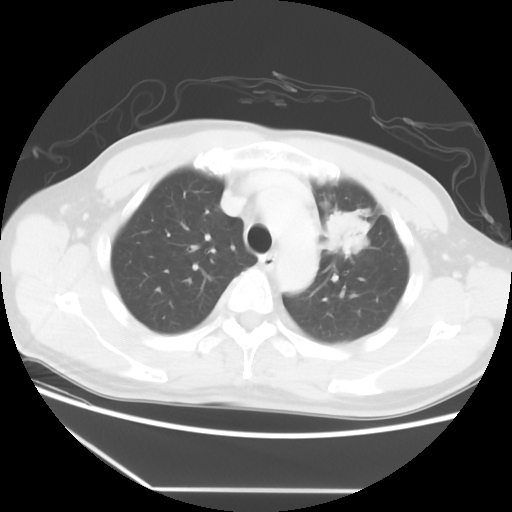
Chest CT, one axial slice; slice 42 of 56 in the series (ordered by position); reconstruction kernel STANDARD; 120 kVp; lung window (W 1500 / L -600 HU); 5 mm slice thickness; 512 × 512 image matrix, field of view 373 × 373 mm. Patient: male, 53 years. Case-level facts recorded for this patient, not image findings: clinical TNM (as recorded): T2a N1 M1b.
Annotated regions visible in this slice (bounding box drawn by a radiologist):
- lung tumour (recorded histology: adenocarcinoma): bounding box <319,206,370,256> (left, top, right, bottom; pixels)